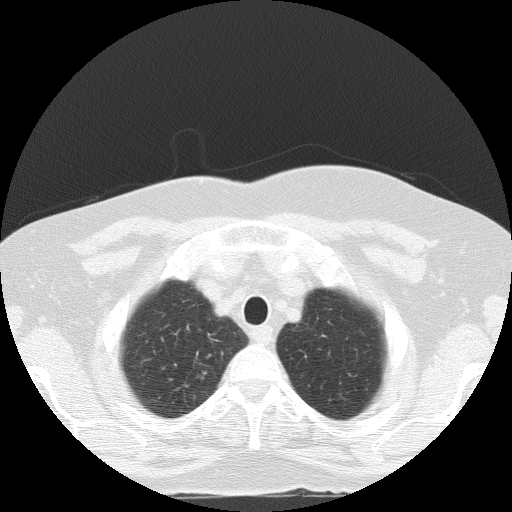
Low-dose screening chest CT, one axial slice; slice 118 of 133 in the series (ordered by position); reconstruction kernel FC51; lung window (W 1500 / L -600 HU); 2 mm slice thickness; 512 × 512 image matrix.
Outlined on this slice (outlined manually by an expert reader):
- lesion 1 (tumor, upper lobe of right lung): bounding box [x1, y1, x2, y2] px = [209, 354, 211, 356]